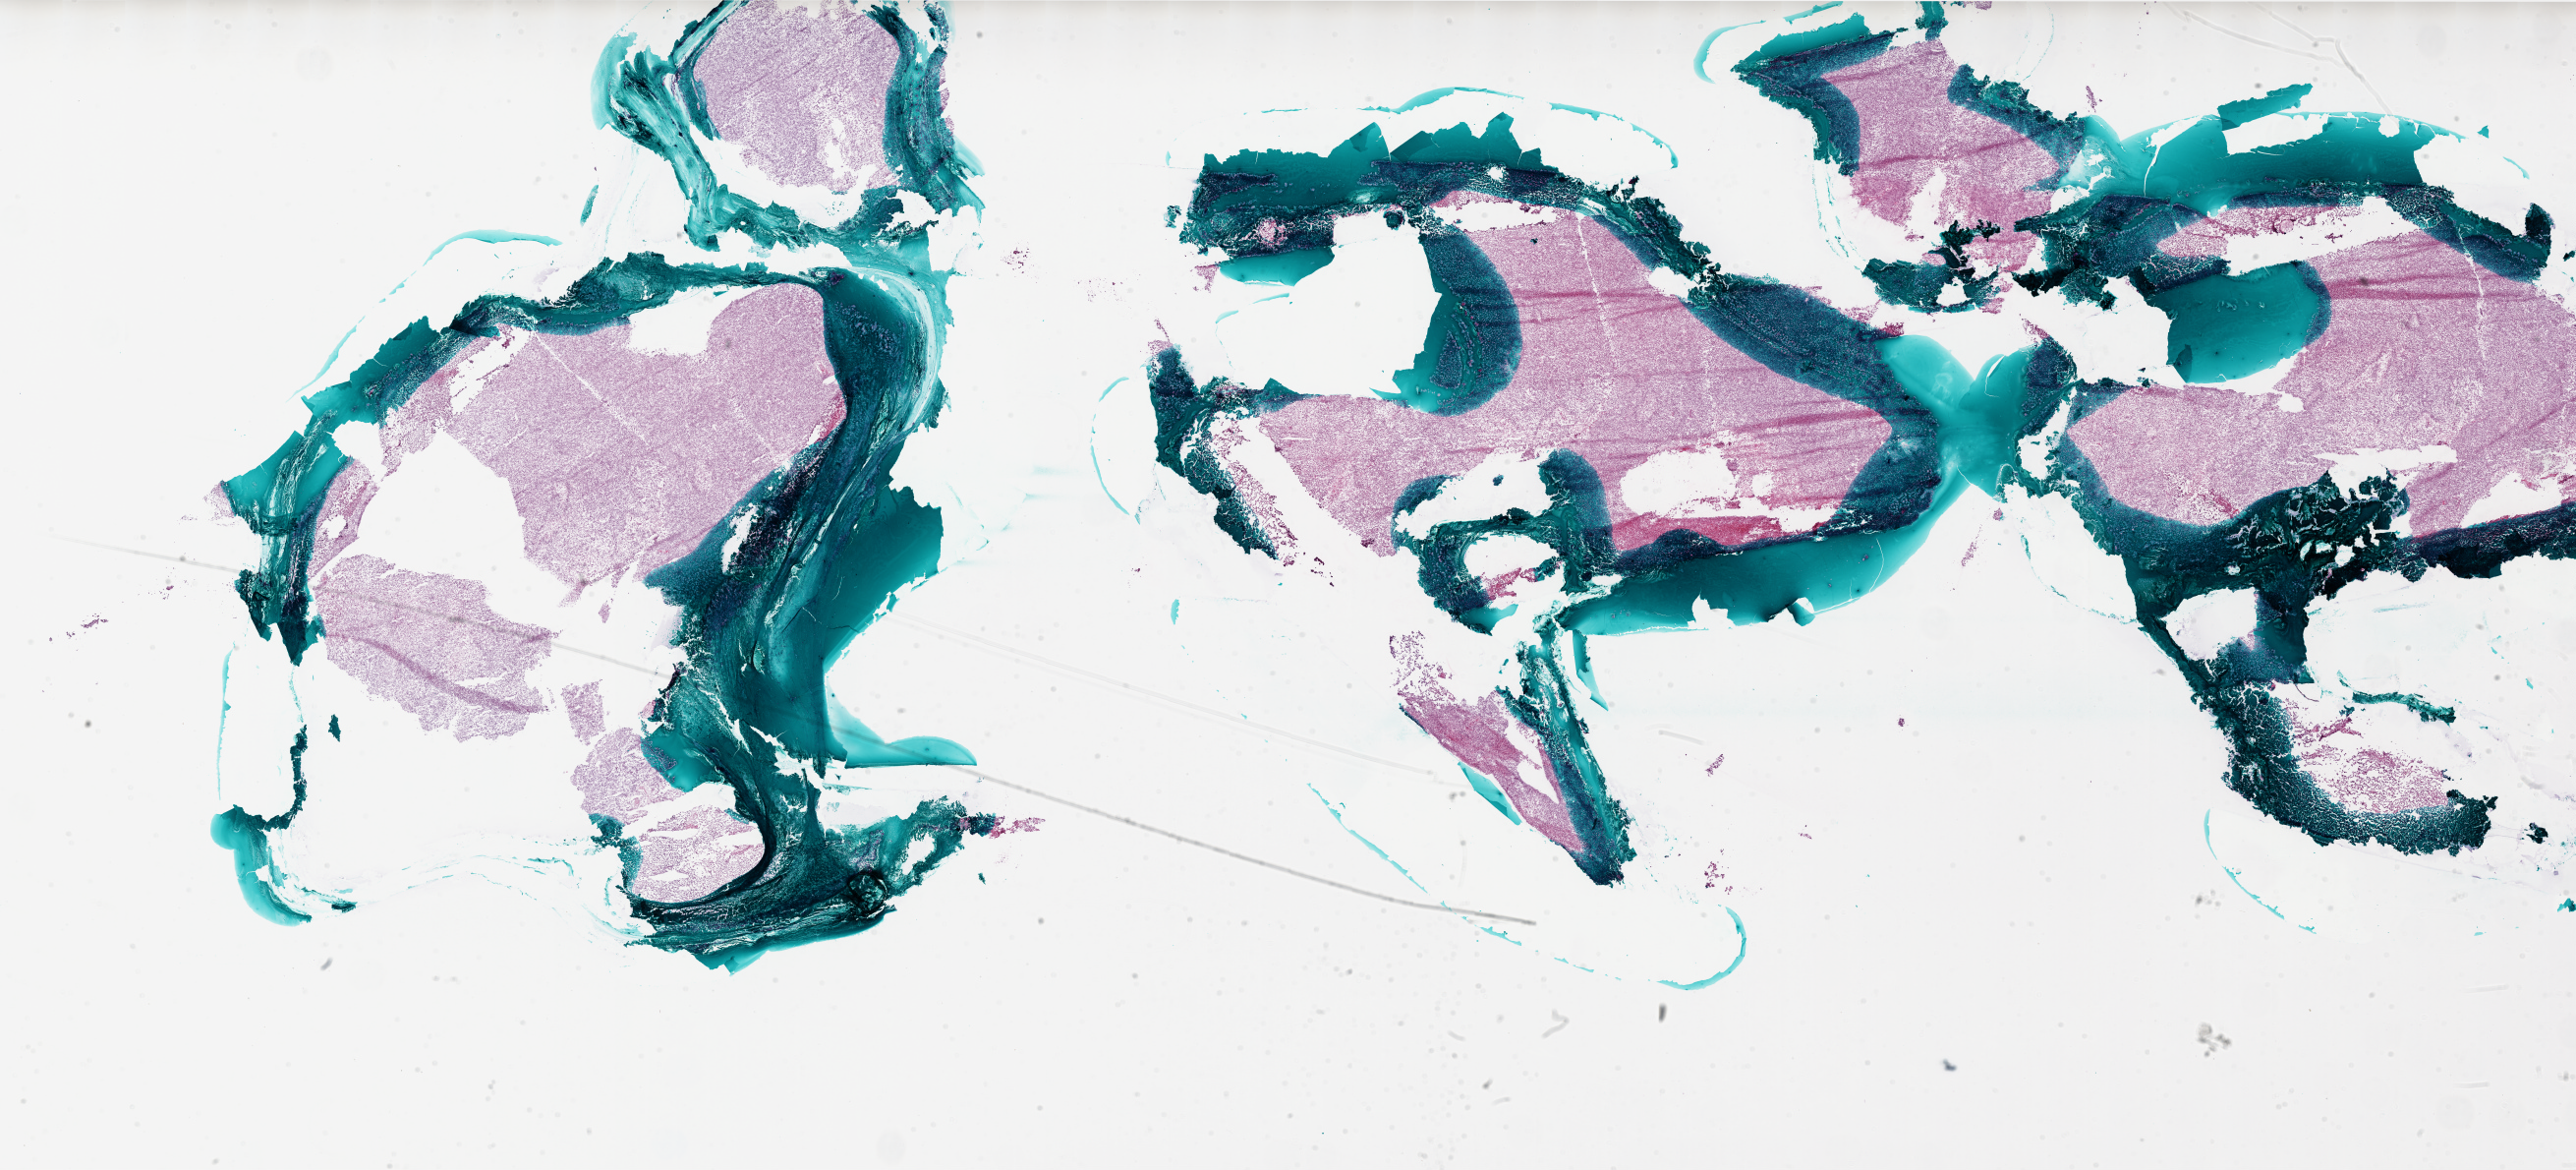
Digitized Hematoxylin and eosin (H&E) stained tissue section (whole slide) — a low-resolution overview of the entire scanned area, about 42.0 x 19.0 mm (from a 20x scan); frozen section from the bottom of the tissue portion; primary tumour sample from the brain. Male patient; age at initial diagnosis 39 years. Pathologist review of this section (percent, as recorded): tumour cells 80%, tumour nuclei 100%.
Pathologic diagnosis: Glioblastoma.